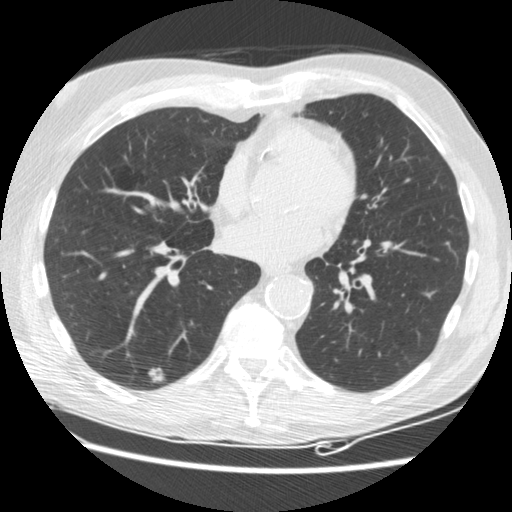
Axial slice from a low-dose chest CT screening exam, third screening round (two years after baseline), lung window (W 1500 / L -600 HU), 2.5 mm slice thickness, standard (soft-tissue) reconstruction kernel (STANDARD), slice 99 of 176 in the series, 512 × 512 image matrix, field of view 347 × 347 mm. Male participant, aged 62 years at enrolment. Current smoker at enrolment.
- Expert reader's lesion annotation, bounding box [x1, y1, x2, y2] px = [140, 356, 180, 395].
- The screening reader recorded 3 non-calcified nodules or masses ≥4 mm on this exam (right lower lobe, right lower lobe, right lower lobe); which of them this box marks is not recorded.
- Official screen result: positive, other.
- Lung cancer was diagnosed 33 days after this screen: adenocarcinoma, NOS, right lower lobe, moderately differentiated (G2), stage IIIB (AJCC 6th edition), 15 mm at pathology.